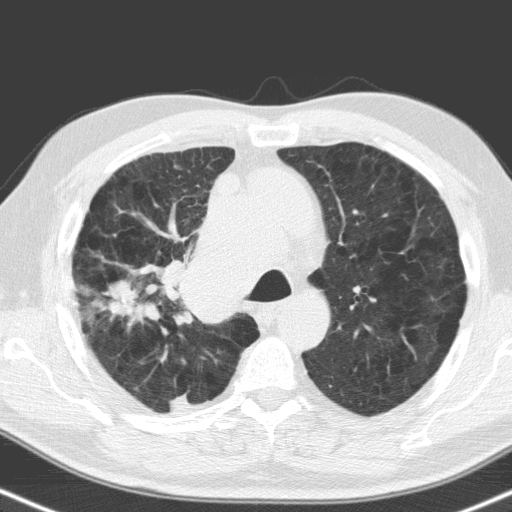
Chest CT (low-dose screening protocol), one axial image. First (baseline) screen. Lung window (W 1500 / L -600 HU). Standard (soft-tissue) reconstruction kernel (C). 512 × 512 image matrix. Male participant, aged 71 years at enrolment. Former smoker at enrolment.
Lesion marked by an expert reader, bounding box (x1, y1, x2, y2) in pixels: (95, 273, 175, 336). The screening reader recorded 2 non-calcified nodules or masses ≥4 mm on this exam (right upper lobe, right upper lobe); which of them this box marks is not recorded. Official screen result: positive, change unspecified: nodule(s) >= 4 mm or enlarging nodule(s), mass(es), or other non-specific abnormalities suspicious for lung cancer. Later outcome: lung cancer diagnosed 31 days after this screen — small cell carcinoma, NOS, right upper lobe, stage IV (AJCC 6th edition), 40 mm at pathology.